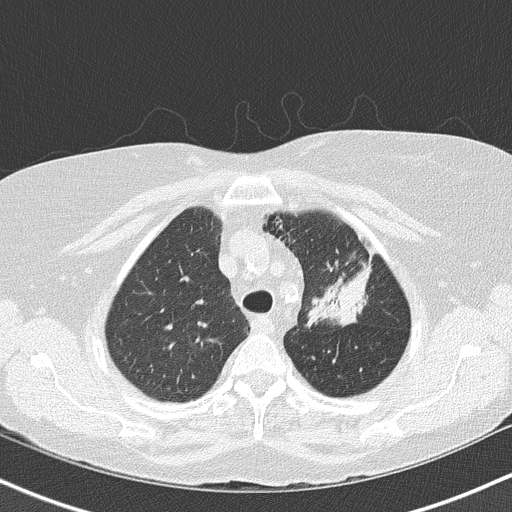
Low-dose screening chest CT, axial slice; third screening round (two years after baseline); lung window (W 1500 / L -600 HU); 2 mm slice thickness; slice 119 of 147 in the series. Female, age 68 years at enrolment. Former smoker at enrolment.
• Lesion marked by an expert reader, bounding box <294,224,381,331> (left, top, right, bottom; pixels).
• Reader record for this screening exam (exam-level; its link to the box is not recorded): non-calcified nodule or mass ≥4 mm, left upper lobe, 5 × 5 mm, poorly defined margins, mixed attenuation, pre-existing on the prior screen: yes; interval growth: yes.
• Official screen result: positive, other.
• Later outcome: lung cancer diagnosed 42 days after this screen — adenocarcinoma, NOS, left upper lobe, poorly differentiated (G3), stage IB (AJCC 6th edition), 50 mm at pathology.